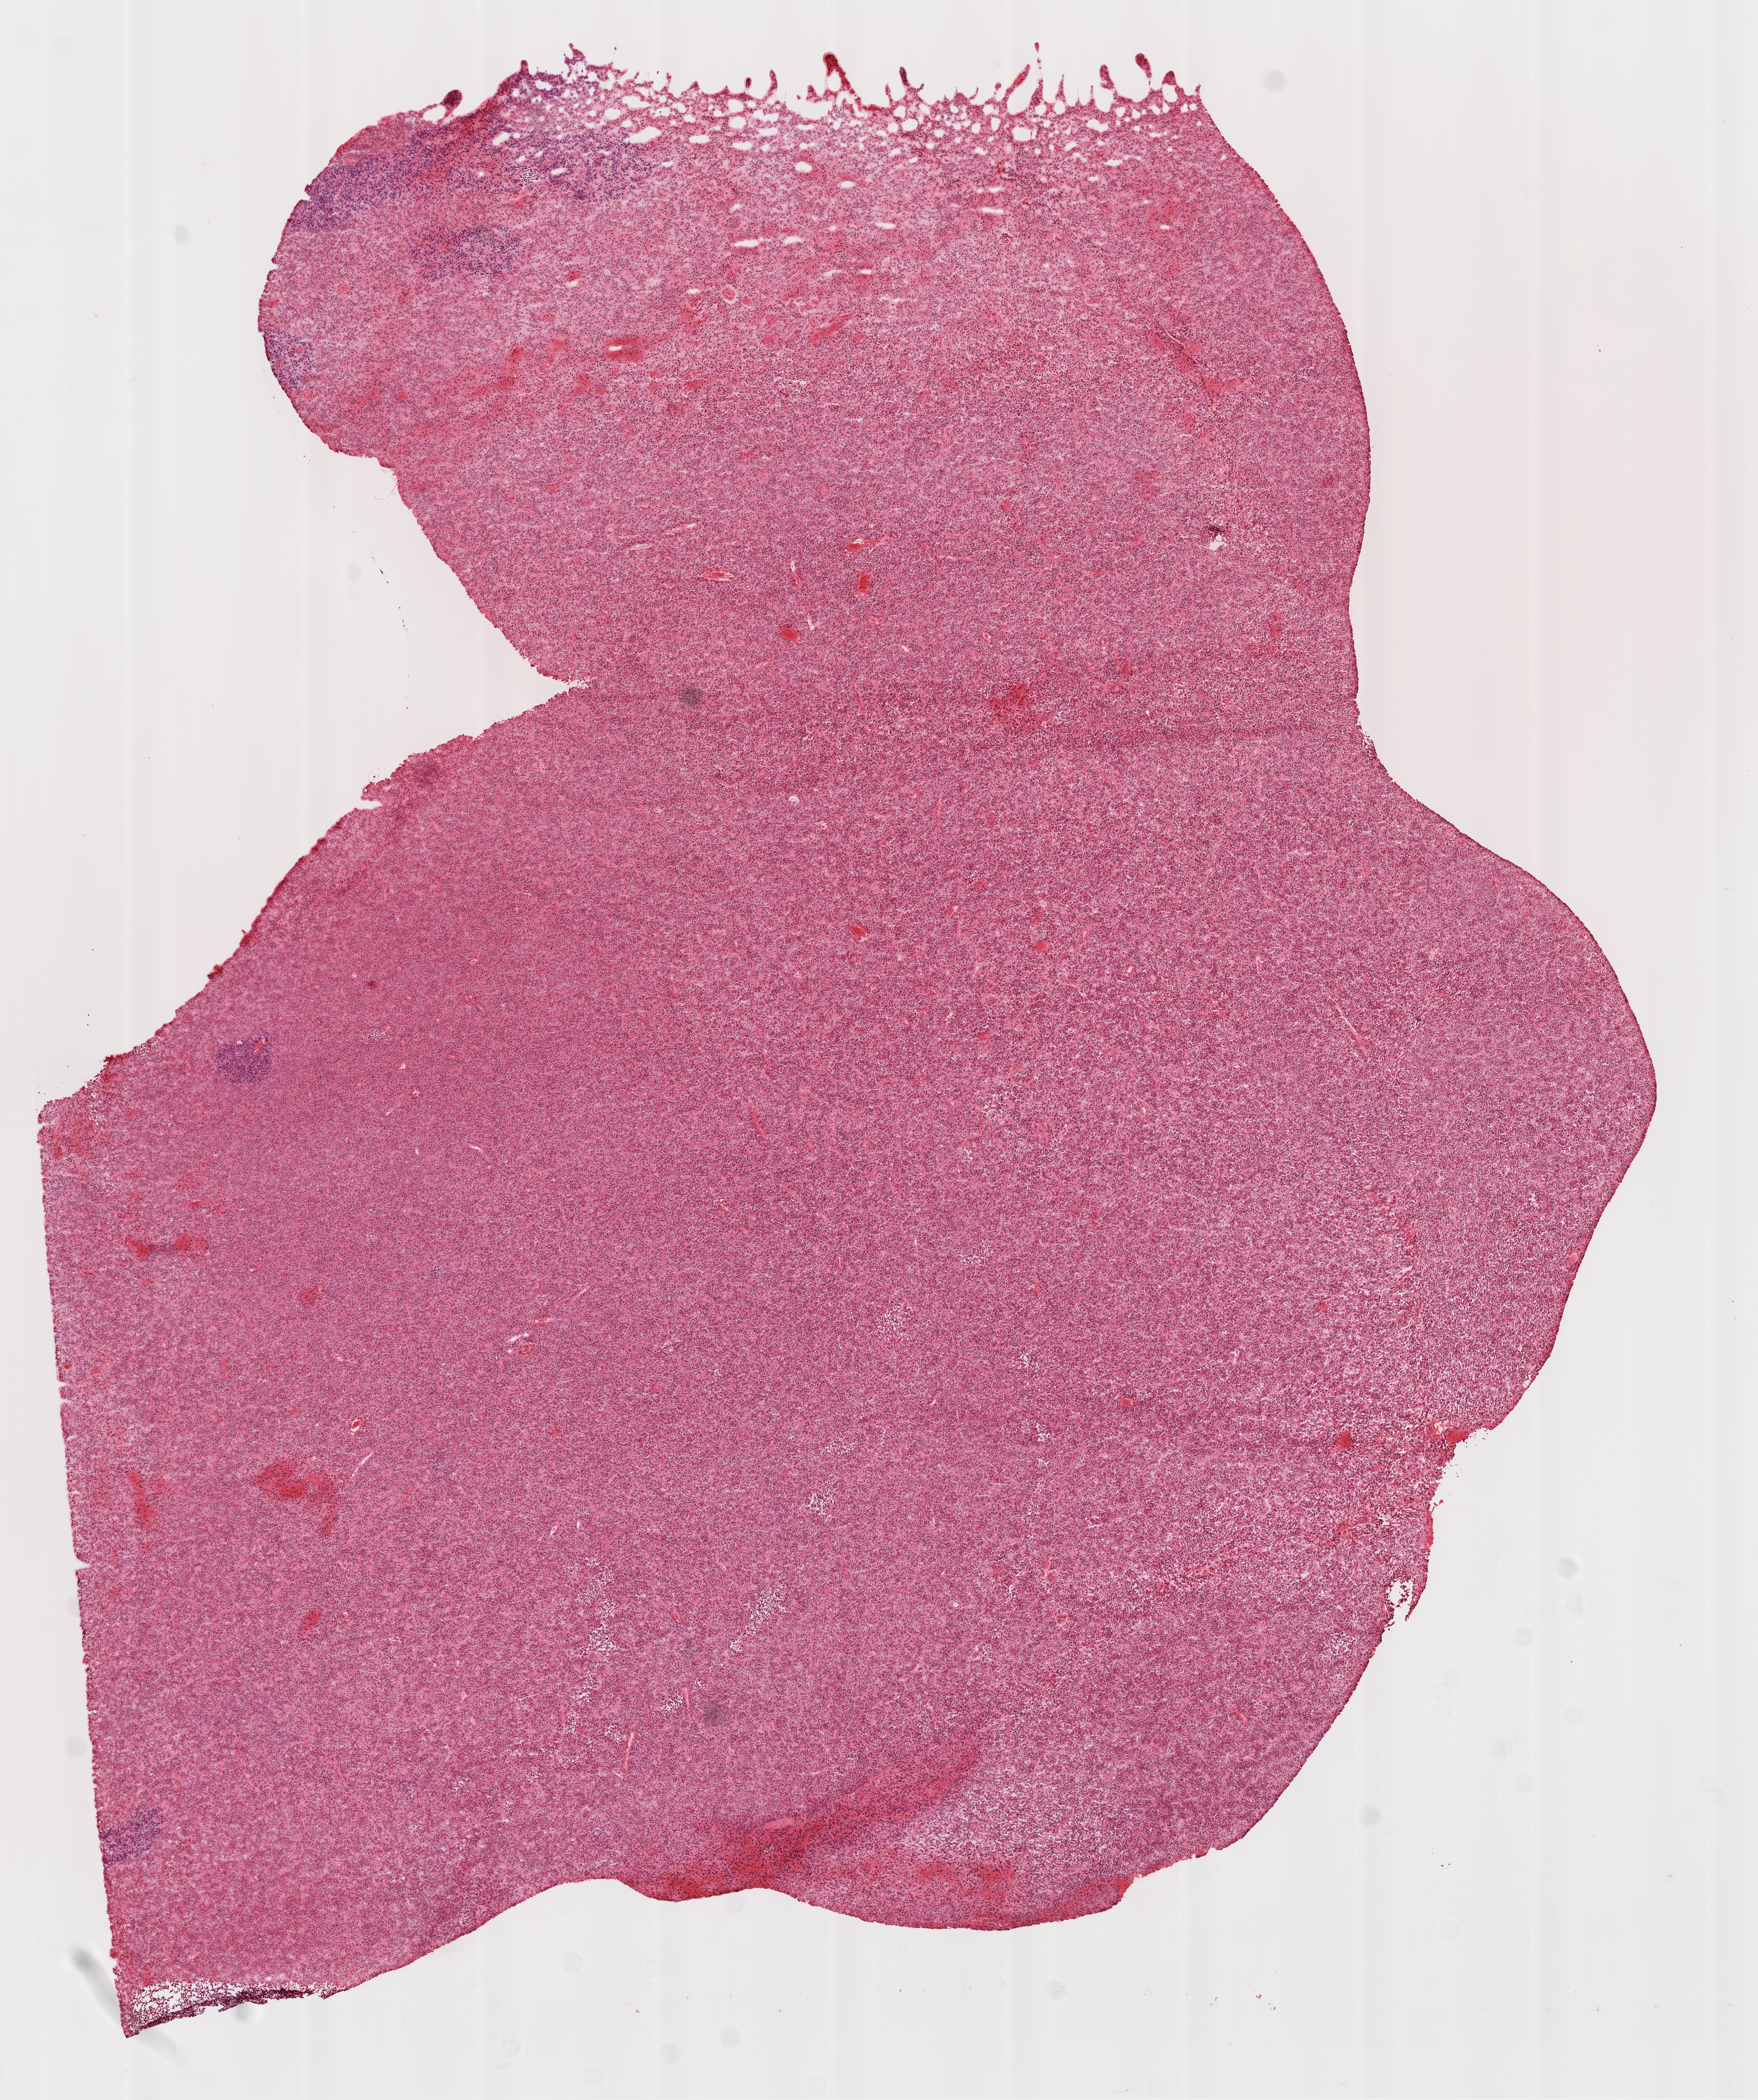
Whole-slide histology image, H&E-stained — shown as a low-resolution overview of the whole scanned area (about 10.0 x 12.0 mm, from a 20x scan), frozen section, primary tumour sample from the brain. Female patient; age at initial diagnosis 34 years. Slide review estimates, as recorded: tumour cells 97%, tumour nuclei 85%, normal cells 0%, stromal cells 0%, necrosis 3%.
Diagnosis: Glioblastoma.